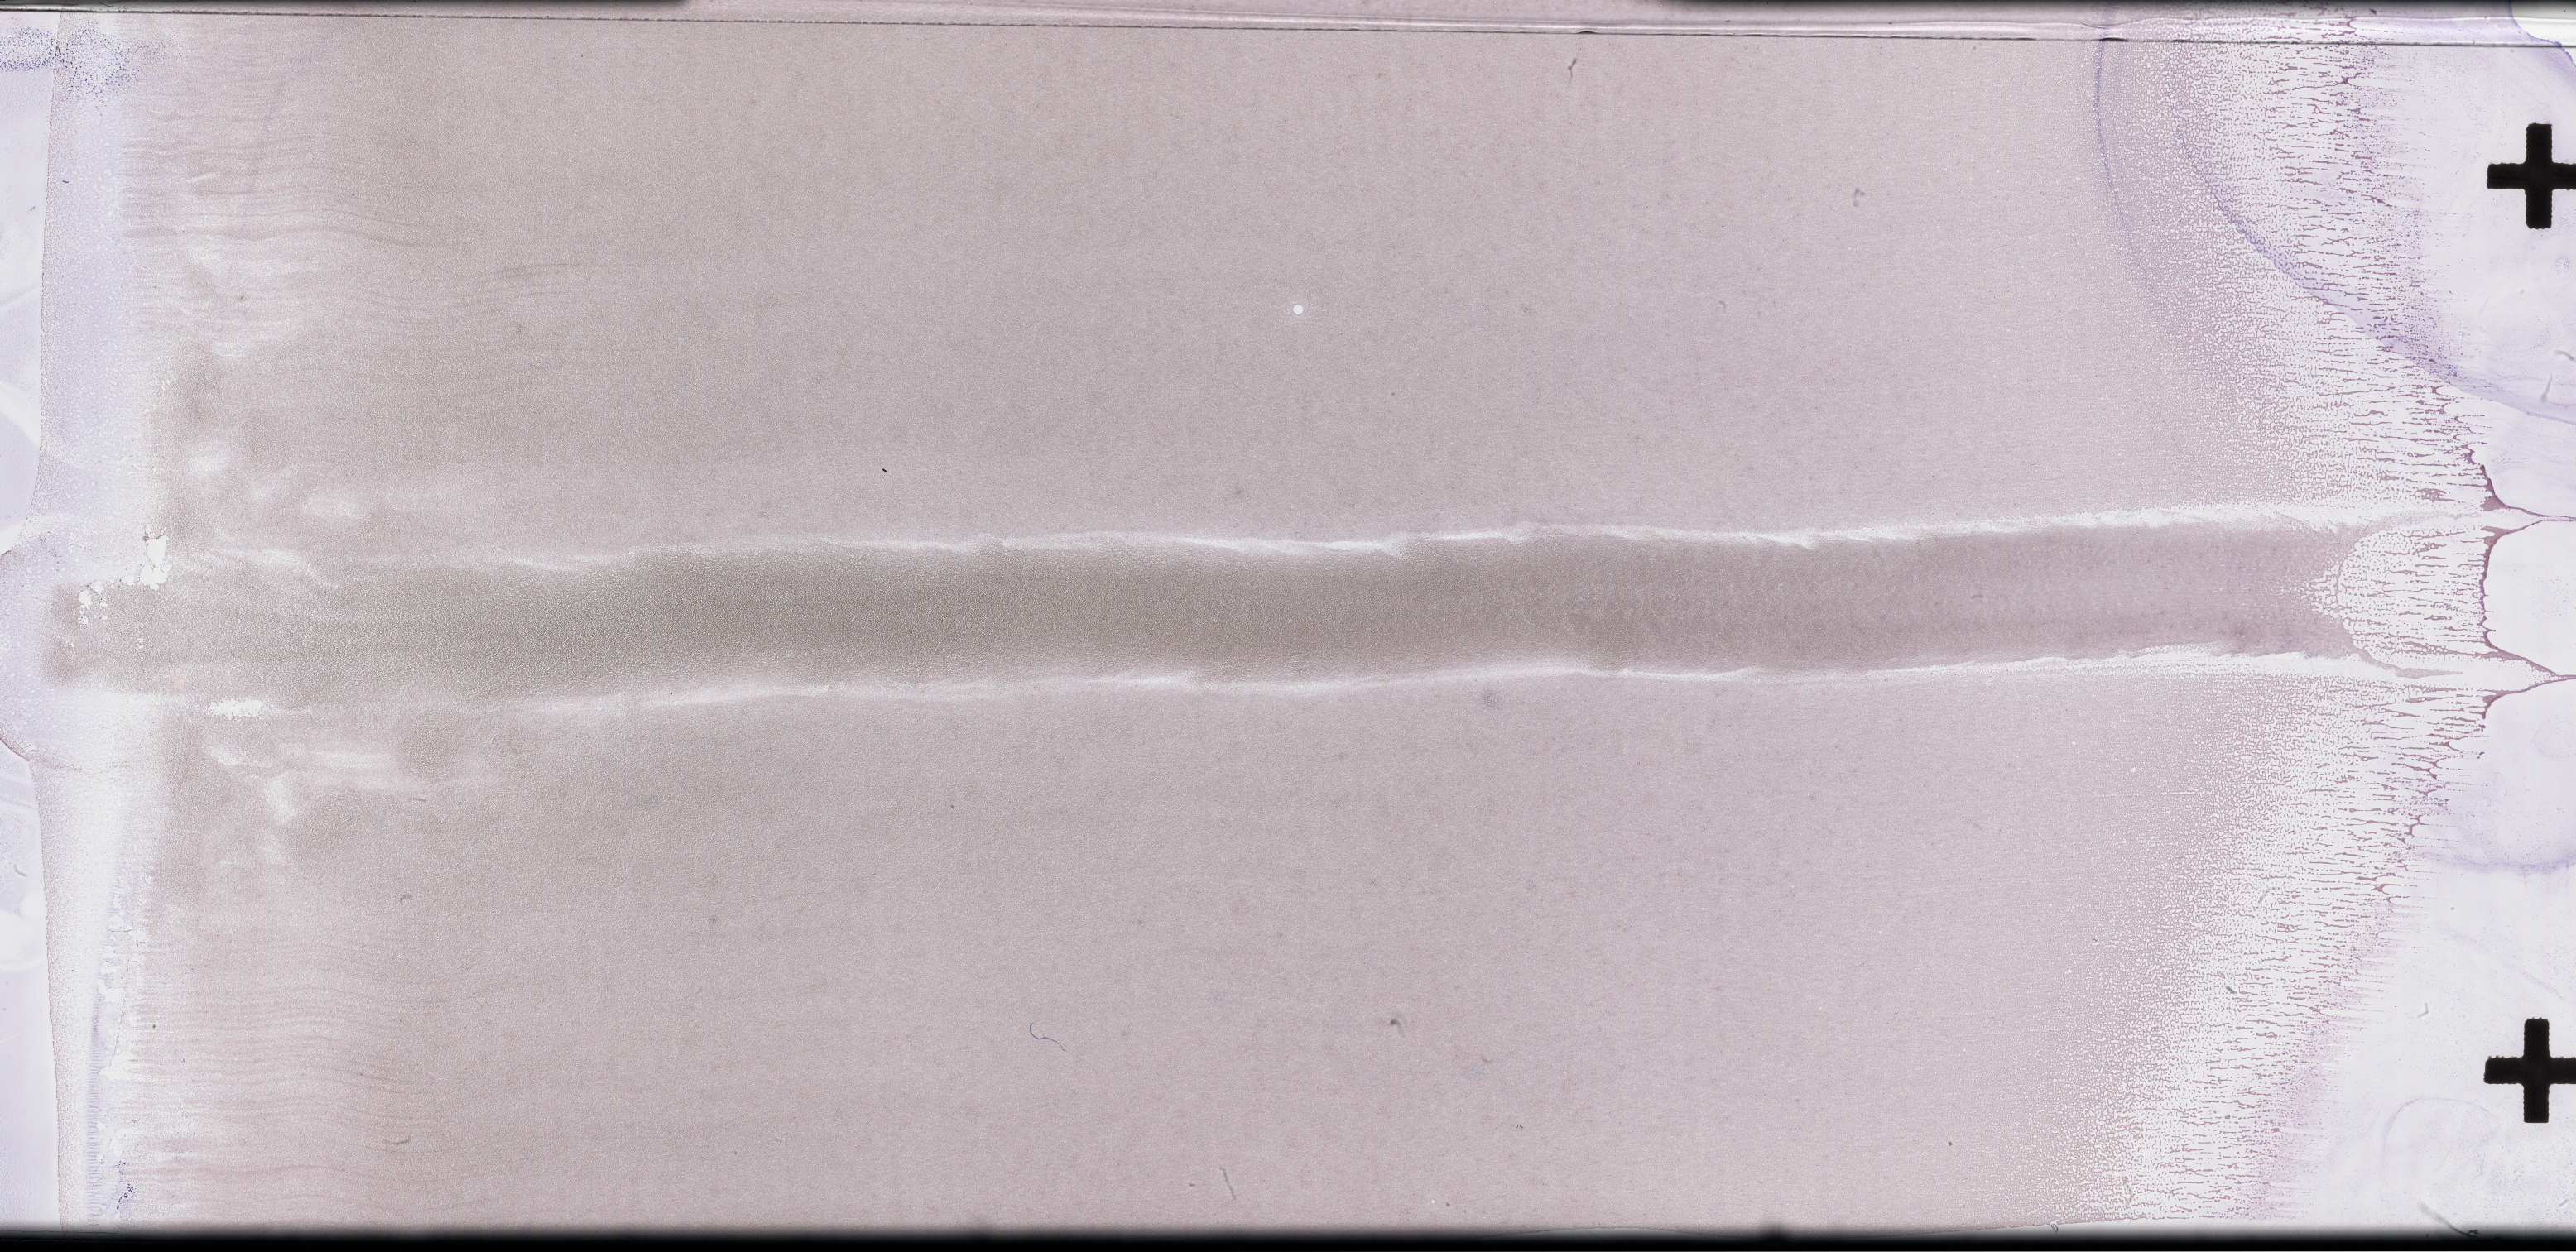
Whole-slide image of a whole blood smear, Wright-Giemsa stain — whole scanned area (about 50.3 x 24.4 mm) shown as a low-resolution overview, collected on treatment. Patient: male.
- from a patient with: Plasma Cell Myeloma